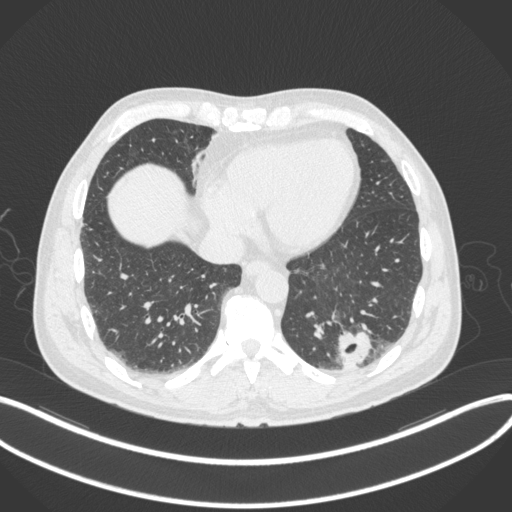
Chest CT, one axial slice. Position 81 of 313 along the scan axis. Reconstruction kernel B31f. Lung window (W 1500 / L -600 HU). 1 mm slice thickness. 512 × 512 image matrix. Male patient, age 54 years. From the clinical record (not read from this slice): clinical TNM (as recorded): T1c N0 M1; histopathological grade: G3.
Outlined on this slice (bounding box drawn by a radiologist):
- lung tumour (recorded histology: adenocarcinoma): bounding box <334,326,372,371> (left, top, right, bottom; pixels)